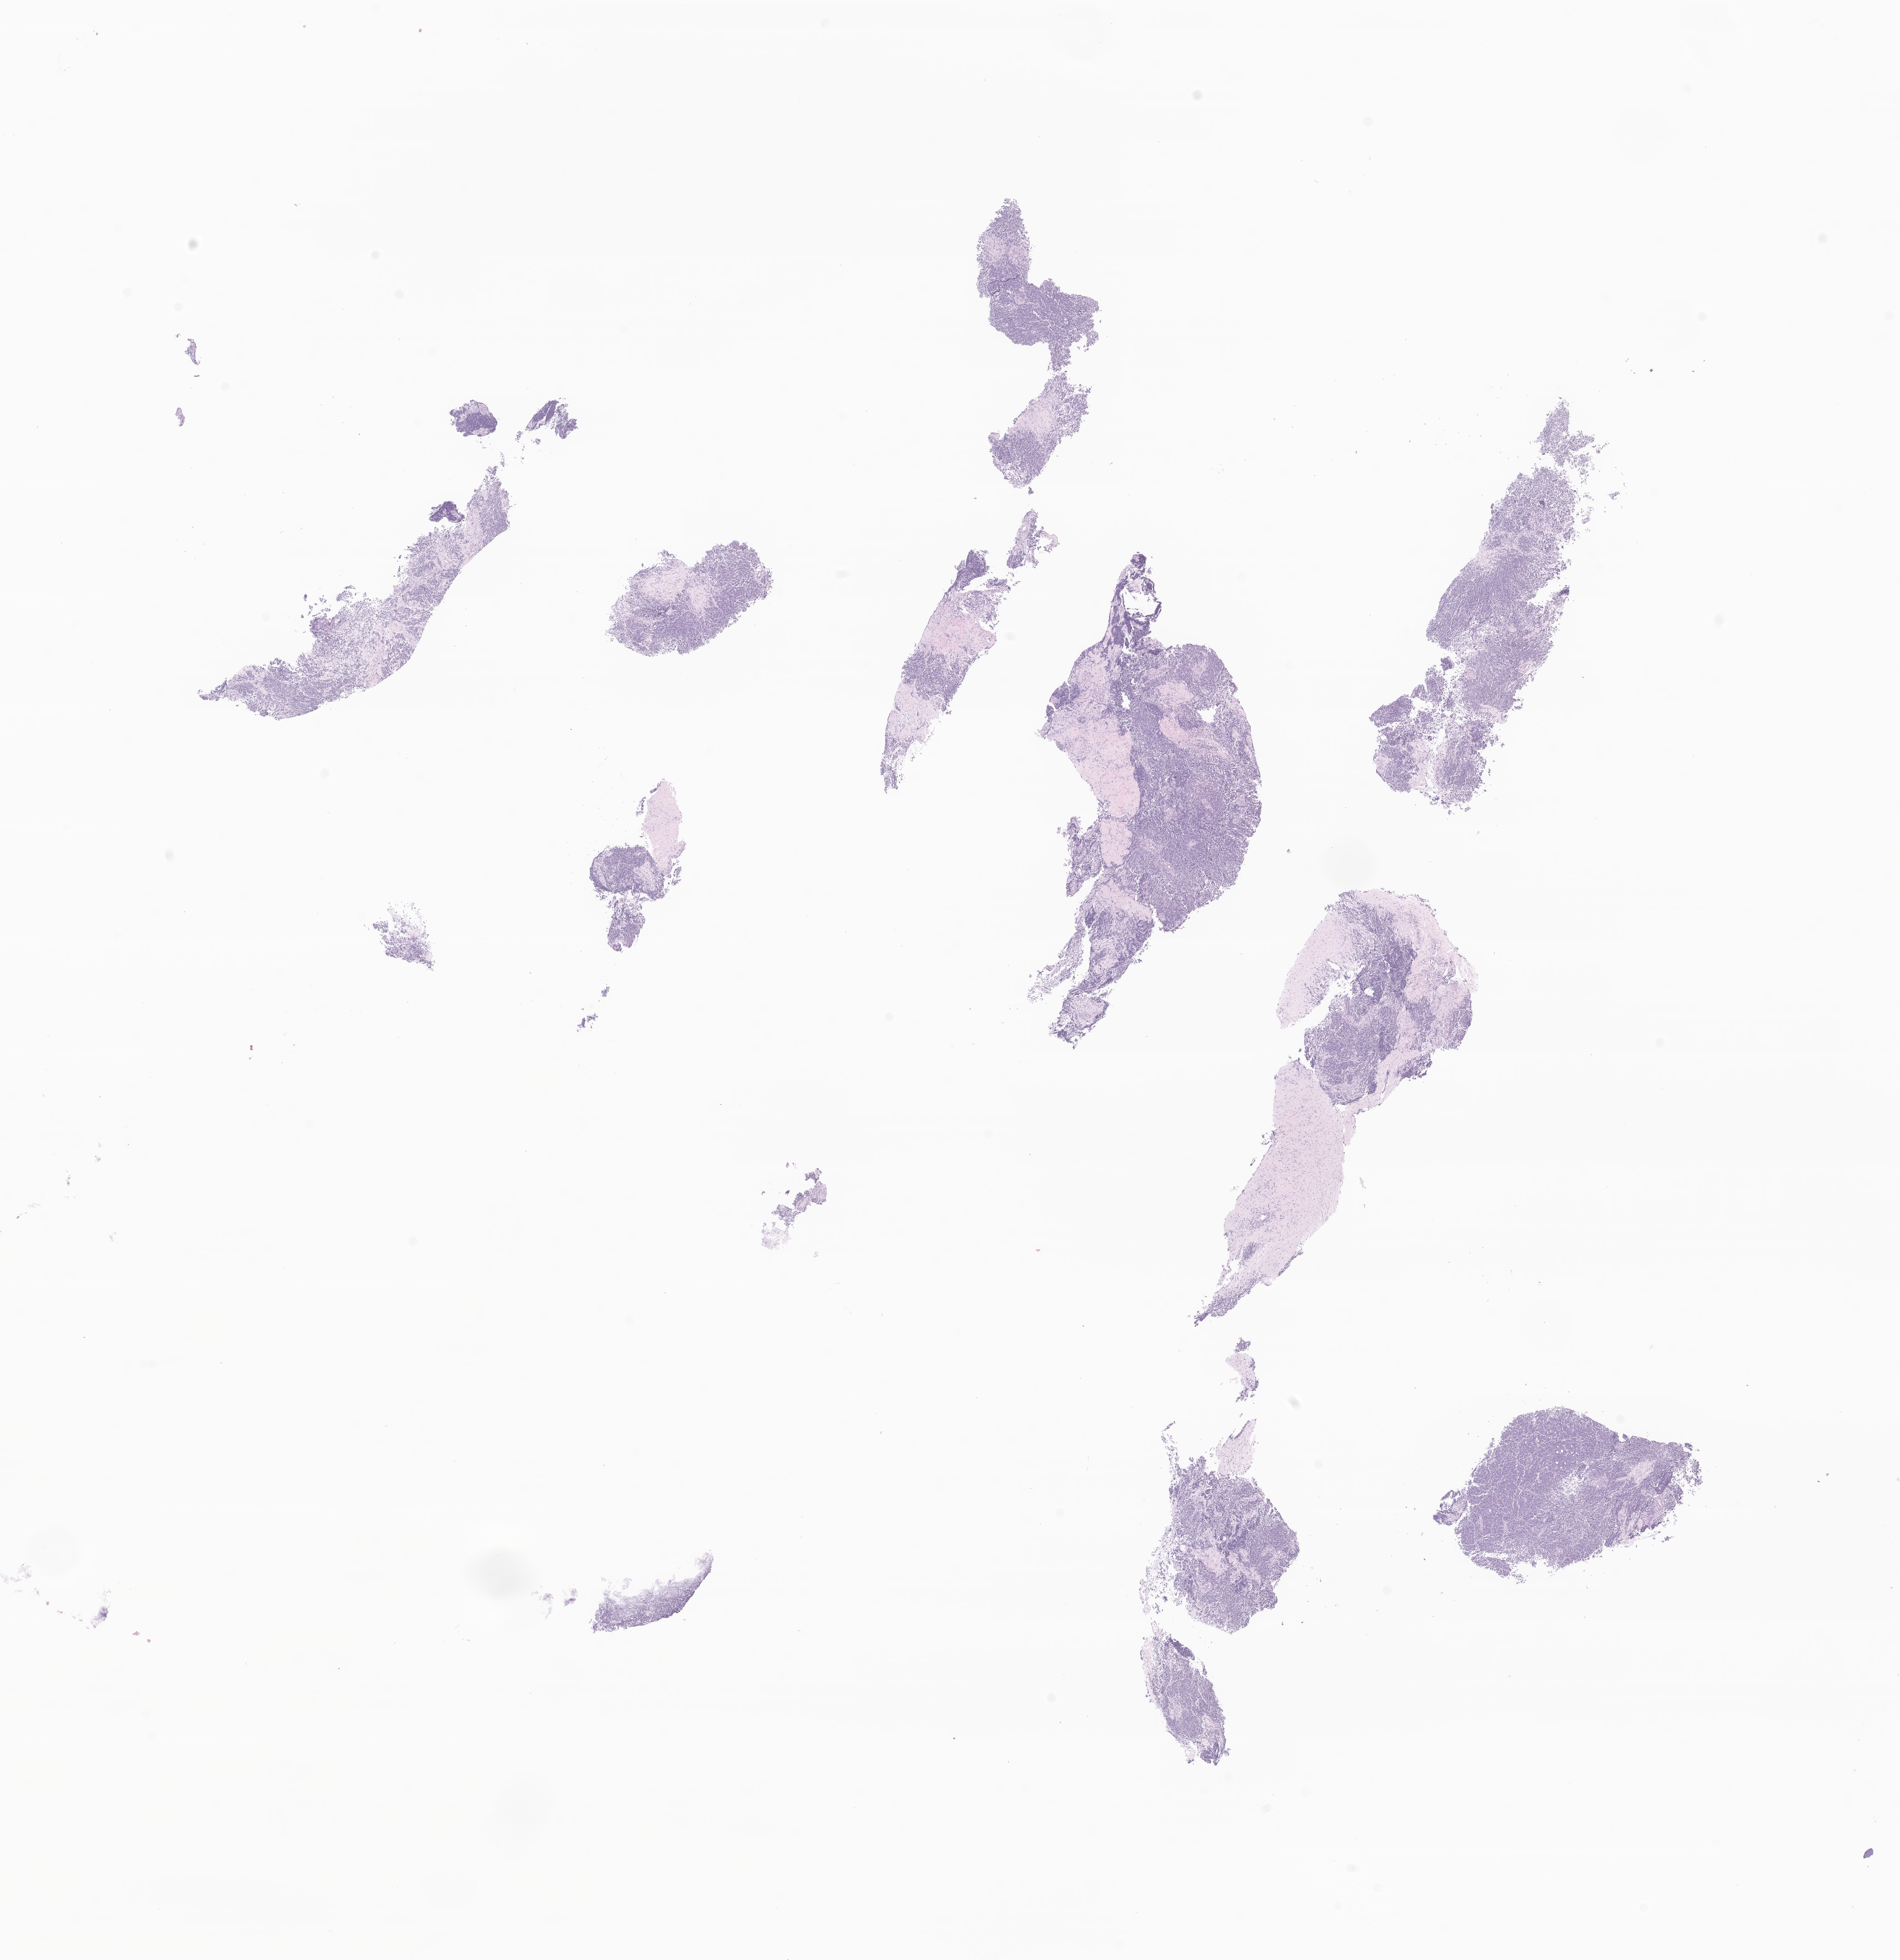
Digitized haematoxylin and eosin-stained section of tumor tissue from the abdomen — whole scanned area (about 17.8 x 18.4 mm) shown as a low-resolution overview. FFPE section. Patient male; age 645 days (about 1.8 years).
Recorded diagnosis: Neuroblastoma, NOS.